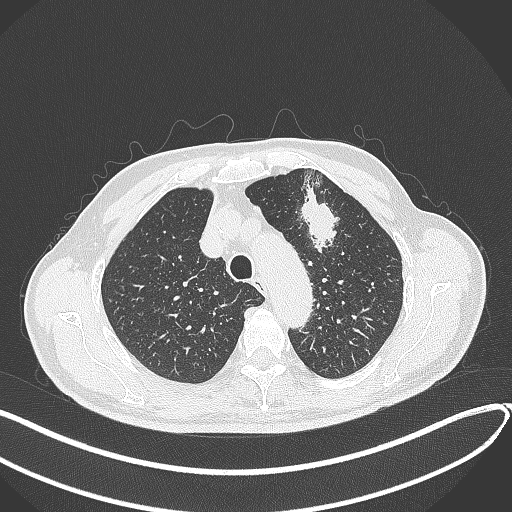
Chest CT, one axial slice; position 327 of 459 along the scan axis; reconstruction kernel B70f; 120 kVp; lung window (W 1500 / L -600 HU); 1 mm slice thickness; 512 × 512 image matrix. Patient: male, 74 years. Case-level facts recorded for this patient, not image findings: clinical TNM (as recorded): T2b N0 M1c.
Outlined on this slice (rectangle marked by the reading radiologist):
- lung tumour (recorded histology: adenocarcinoma): bounding box (x1, y1, x2, y2) in pixels: (294, 185, 345, 257)